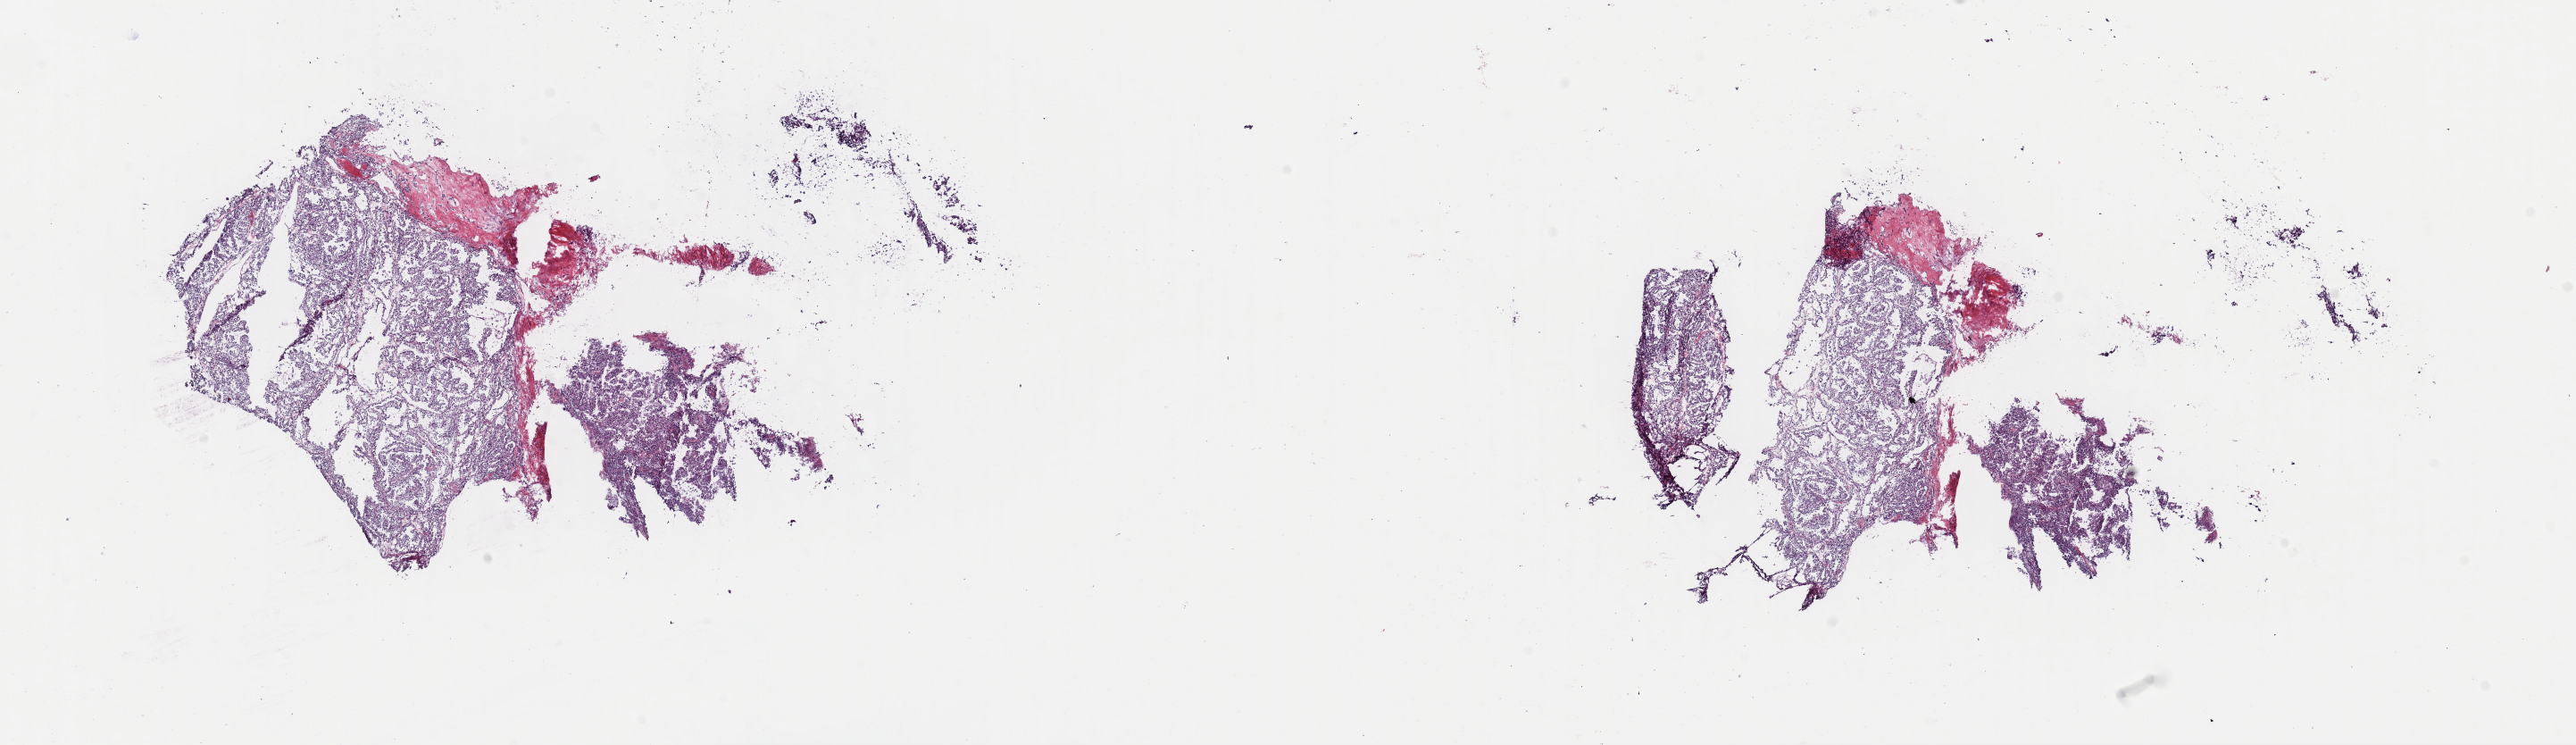
H&E-stained whole-slide image, whole scanned area (about 22.8 x 6.6 mm, from a 40x scan) shown as a low-resolution overview. Frozen section from the top of the tissue portion. Kidney, primary tumour sample. Male patient; age at initial diagnosis 69 years. Histologic grade: G2 (moderately differentiated). Pathologist review of this section (percent, as recorded): tumour cells 90%, tumour nuclei 90%, normal cells 0%, stromal cells 10%, necrosis 0%. Infiltration values recorded for this section: lymphocyte infiltration 0%, monocyte infiltration 0%, neutrophil infiltration 0%.
* histologic diagnosis: Renal cell carcinoma, NOS
* AJCC pathologic stage: III
* laterality: left